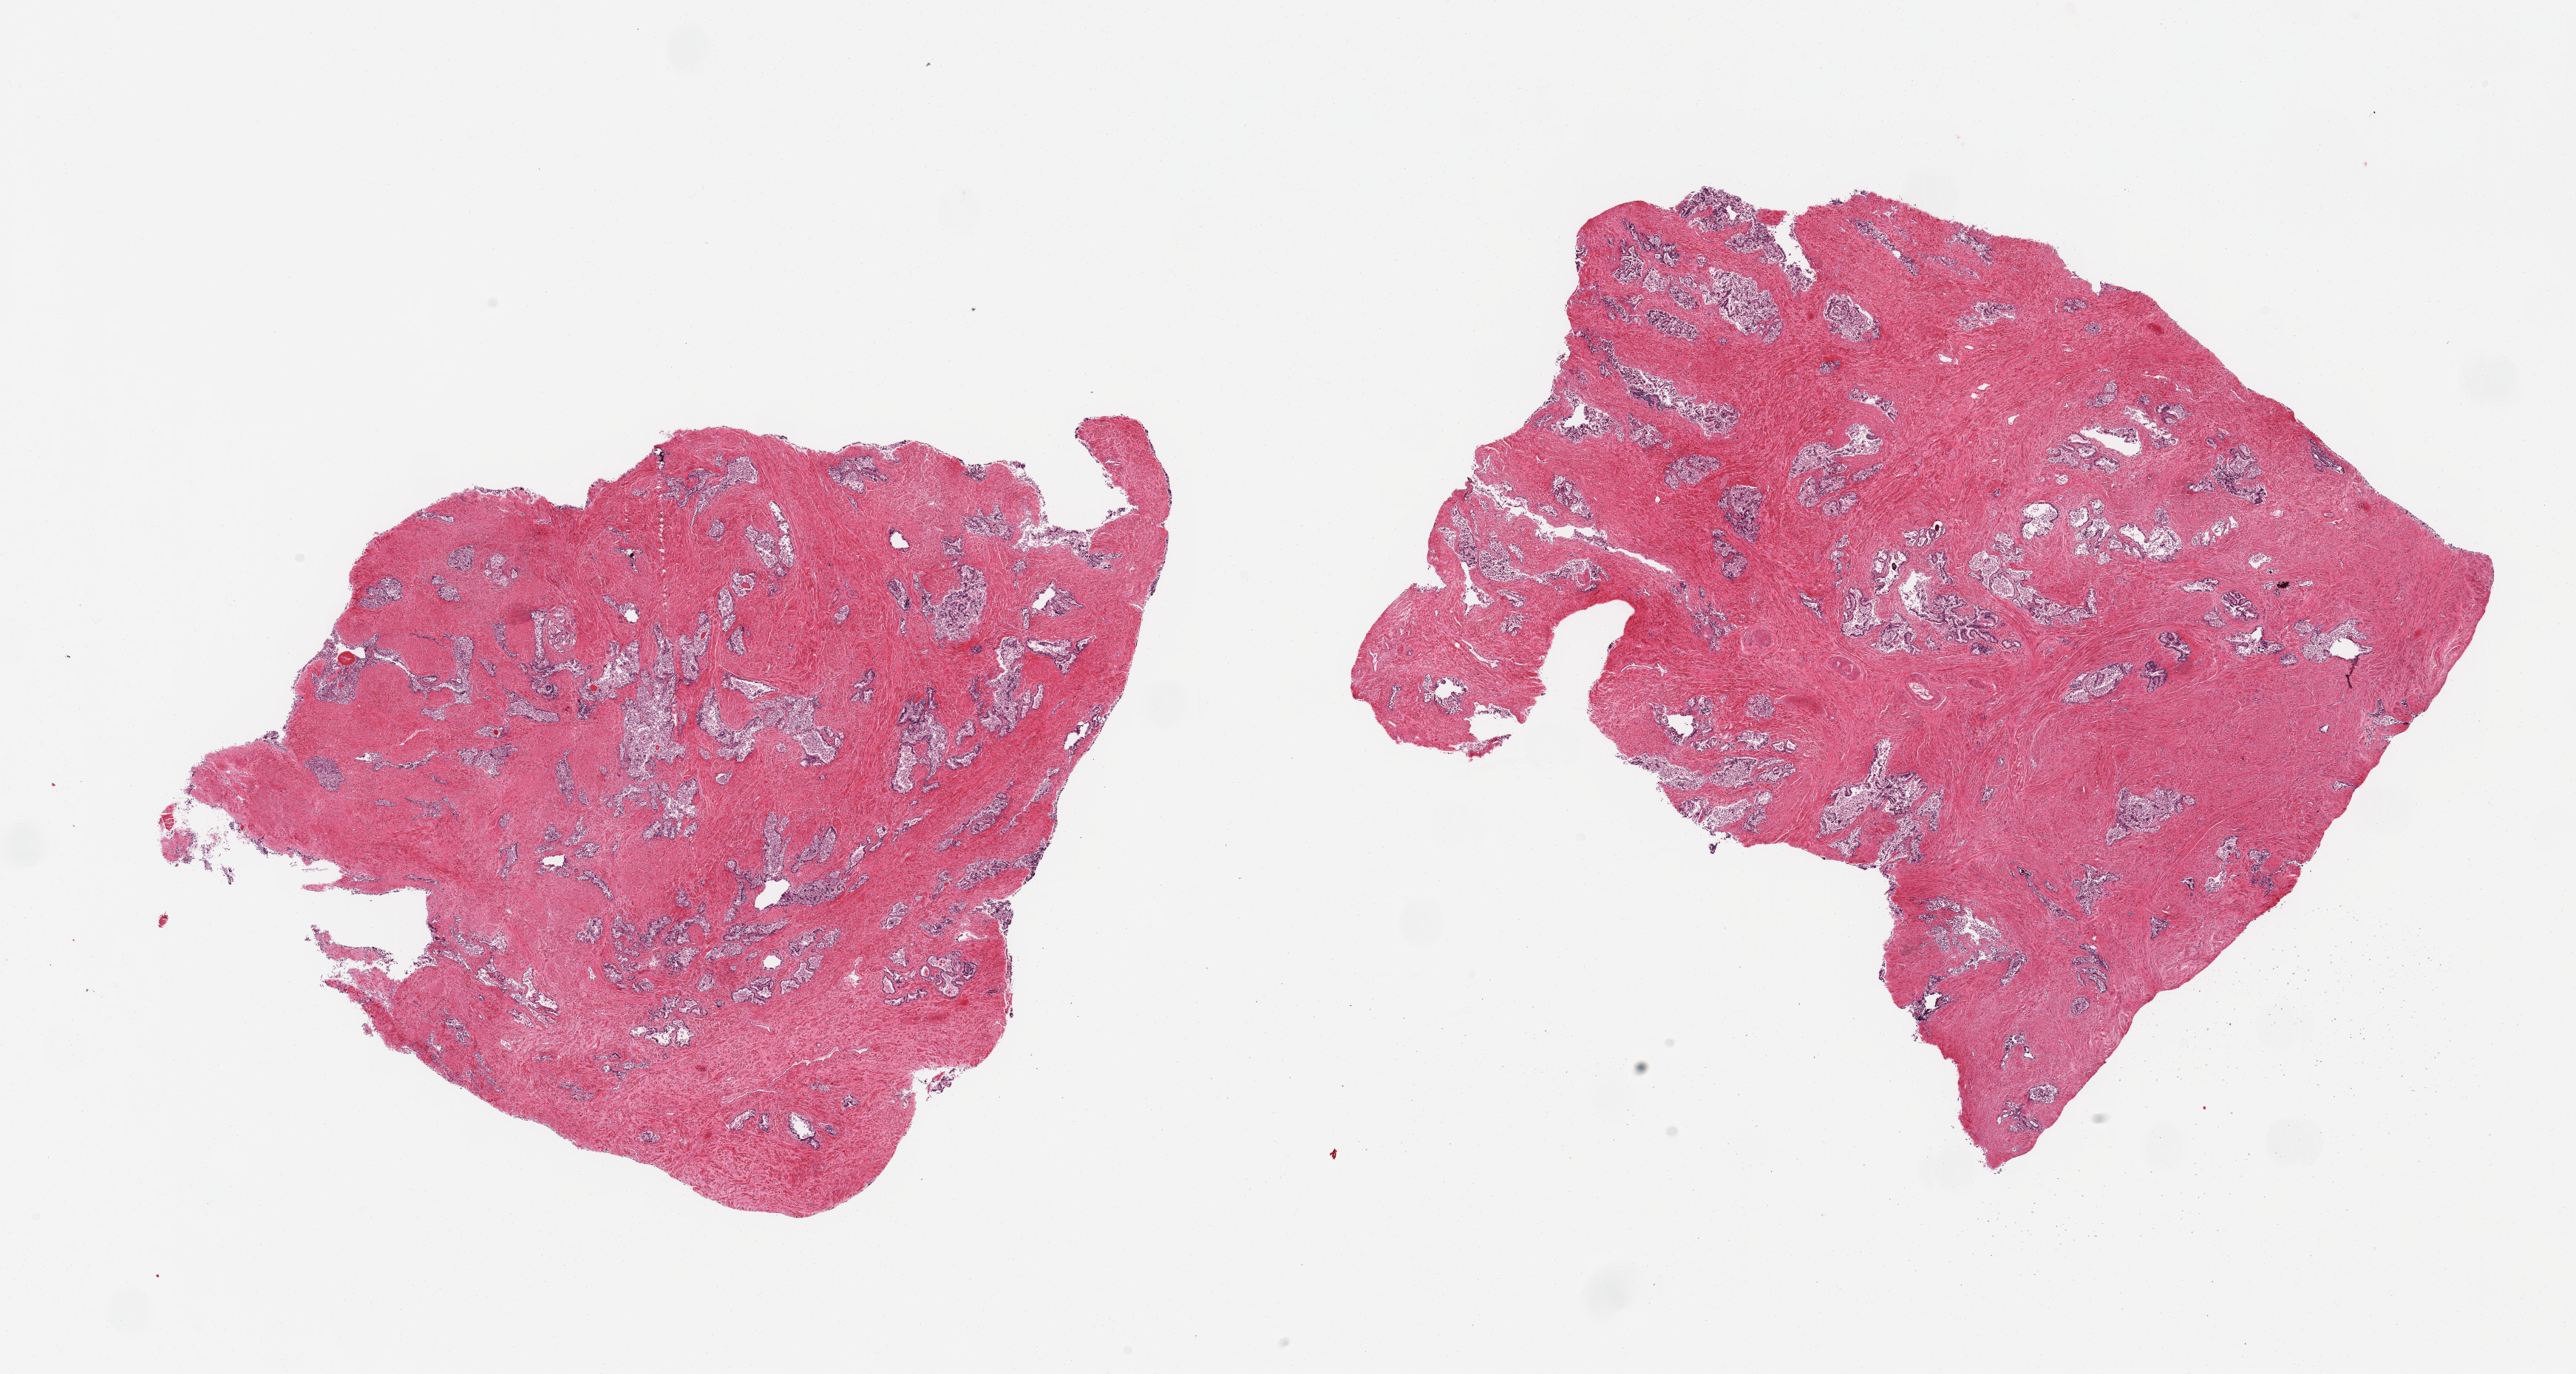
Hematoxylin and eosin (H&E) whole-slide image — a low-resolution overview of the entire scanned area, about 27.6 x 14.7 mm (acquisition: 20x scan). PAXgene-fixed, paraffin-embedded tissue. Sampled site (target tissue): prostate. Donor tissue sample. Donor: male.
- review note (as recorded): 2 pieces; glandular sloughing; stroma intact